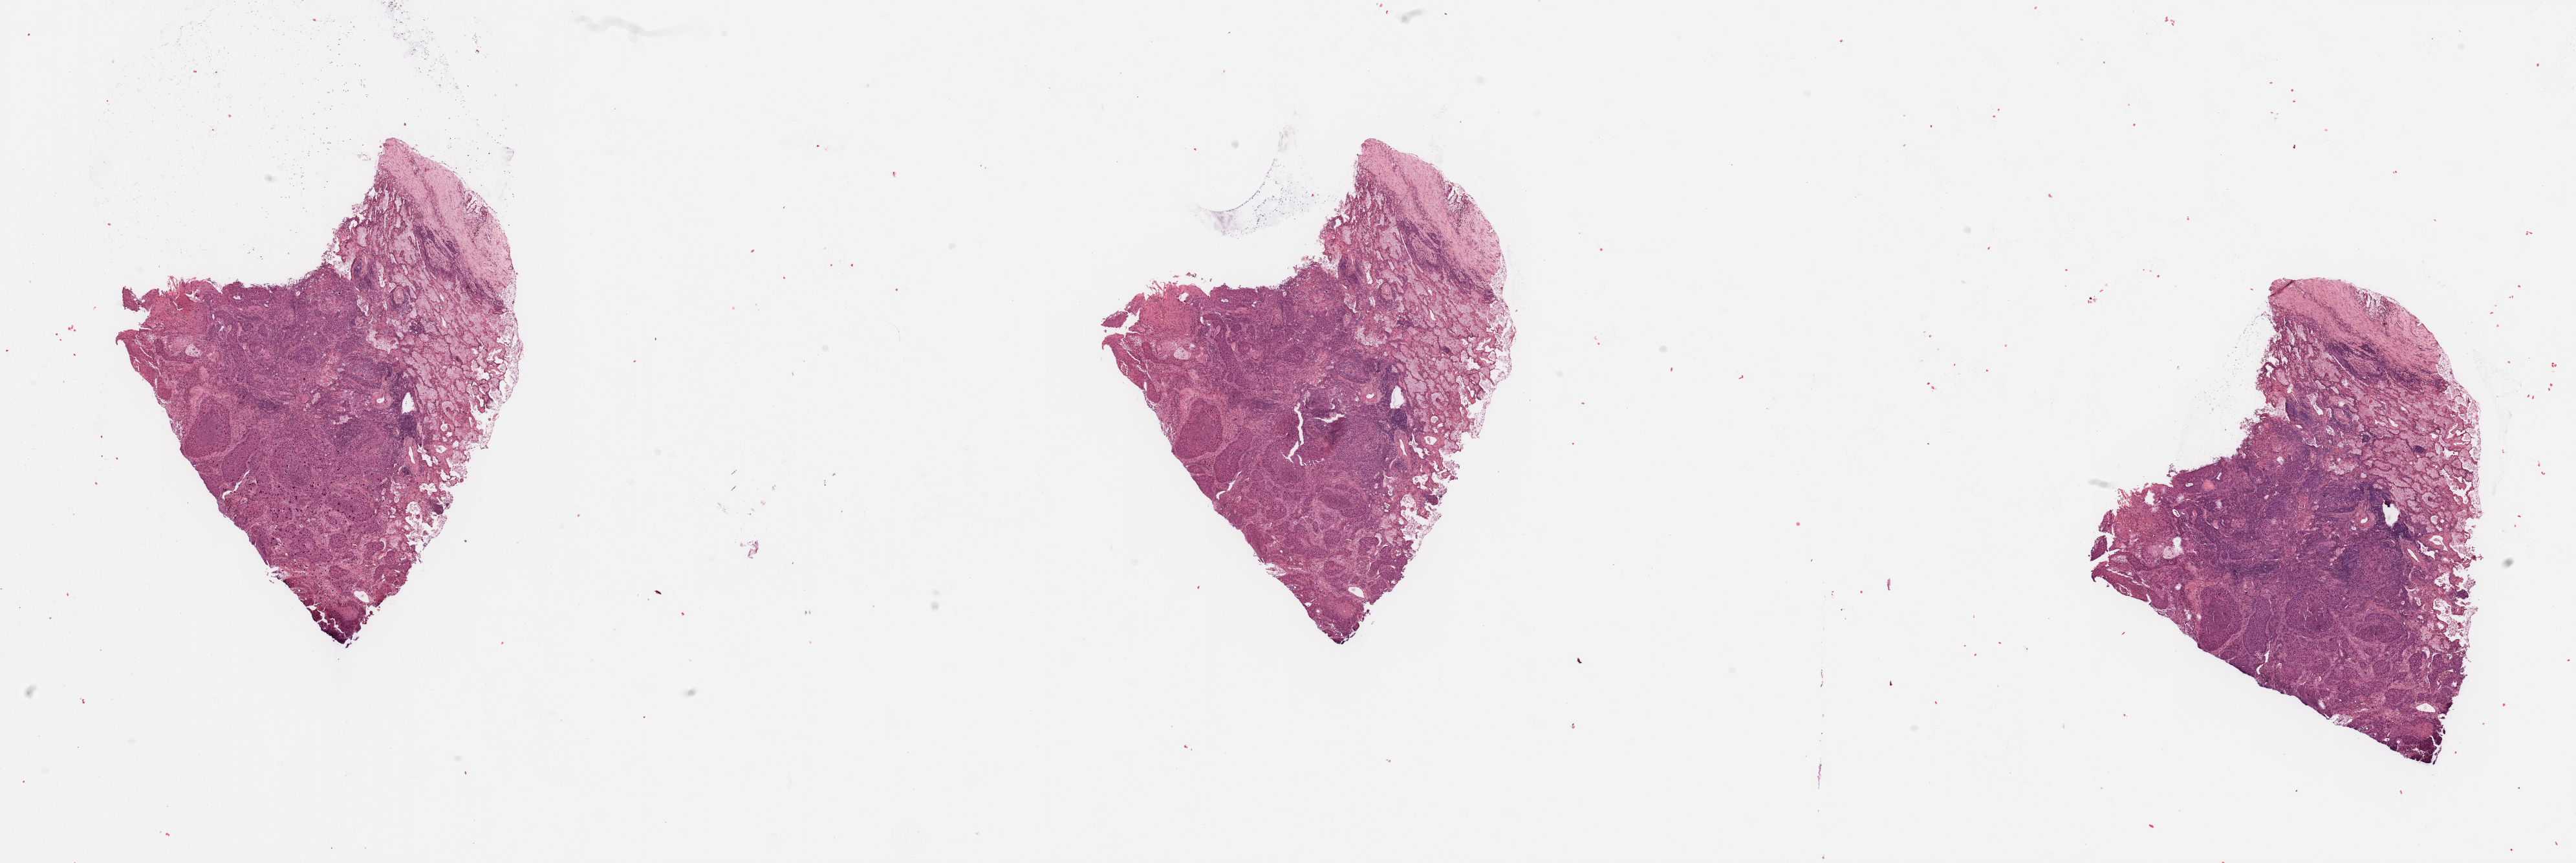
Whole-slide histology image, H&E, low-resolution overview of the scanned area, about 31.5 x 10.6 mm (slide scanned at 20x), tumour tissue sample, sampled site: lung. Female, 64 y/o. Histologic grade: G2 (moderately differentiated). Composition of this section per pathologist review: tumour nuclei 65%, necrosis 5%.
• primary tumour site (as recorded): left upper lobe
• AJCC pathologic stage: IB
• diagnosis: Squamous cell carcinoma, NOS